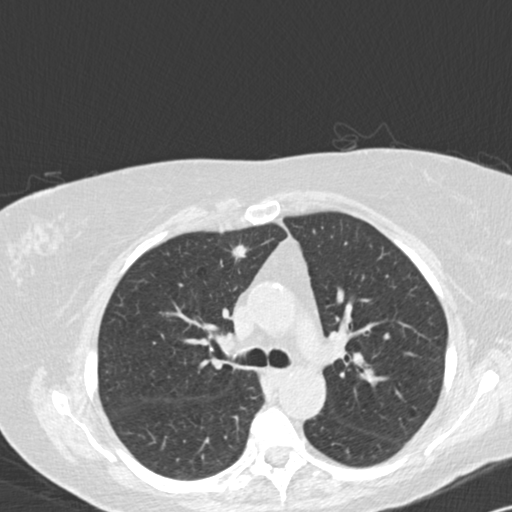
Low-dose screening chest CT, one axial slice. Position 96 of 141 along the scan axis. Reconstruction kernel B30f. 120 kVp. Lung window (W 1500 / L -600 HU). 2 mm slice thickness. 512 × 512 image matrix, field of view 328 × 328 mm.
Outlined on this slice (manually delineated by an expert):
- lesion 1 (tumor, upper lobe of right lung): bounding box [x1, y1, x2, y2] px = [232, 244, 247, 258]